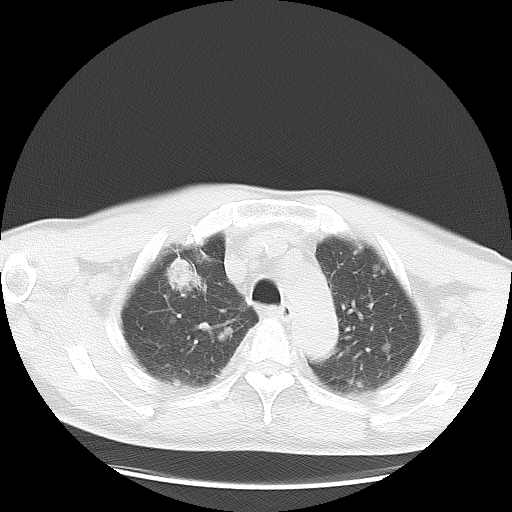
Chest CT, one axial slice. Position 23 of 35 along the scan axis. Reconstruction kernel LUNG. Lung window (W 1500 / L -600 HU). 5 mm slice thickness. 512 × 512 image matrix, field of view 369 × 369 mm. Patient: male, 57 years. Case-level facts recorded for this patient, not image findings: clinical TNM (as recorded): T2 N3 M1a.
Annotated regions visible in this slice (rectangle marked by the reading radiologist):
- lung tumour (recorded histology: adenocarcinoma): bounding box [x1, y1, x2, y2] px = [157, 255, 211, 299]